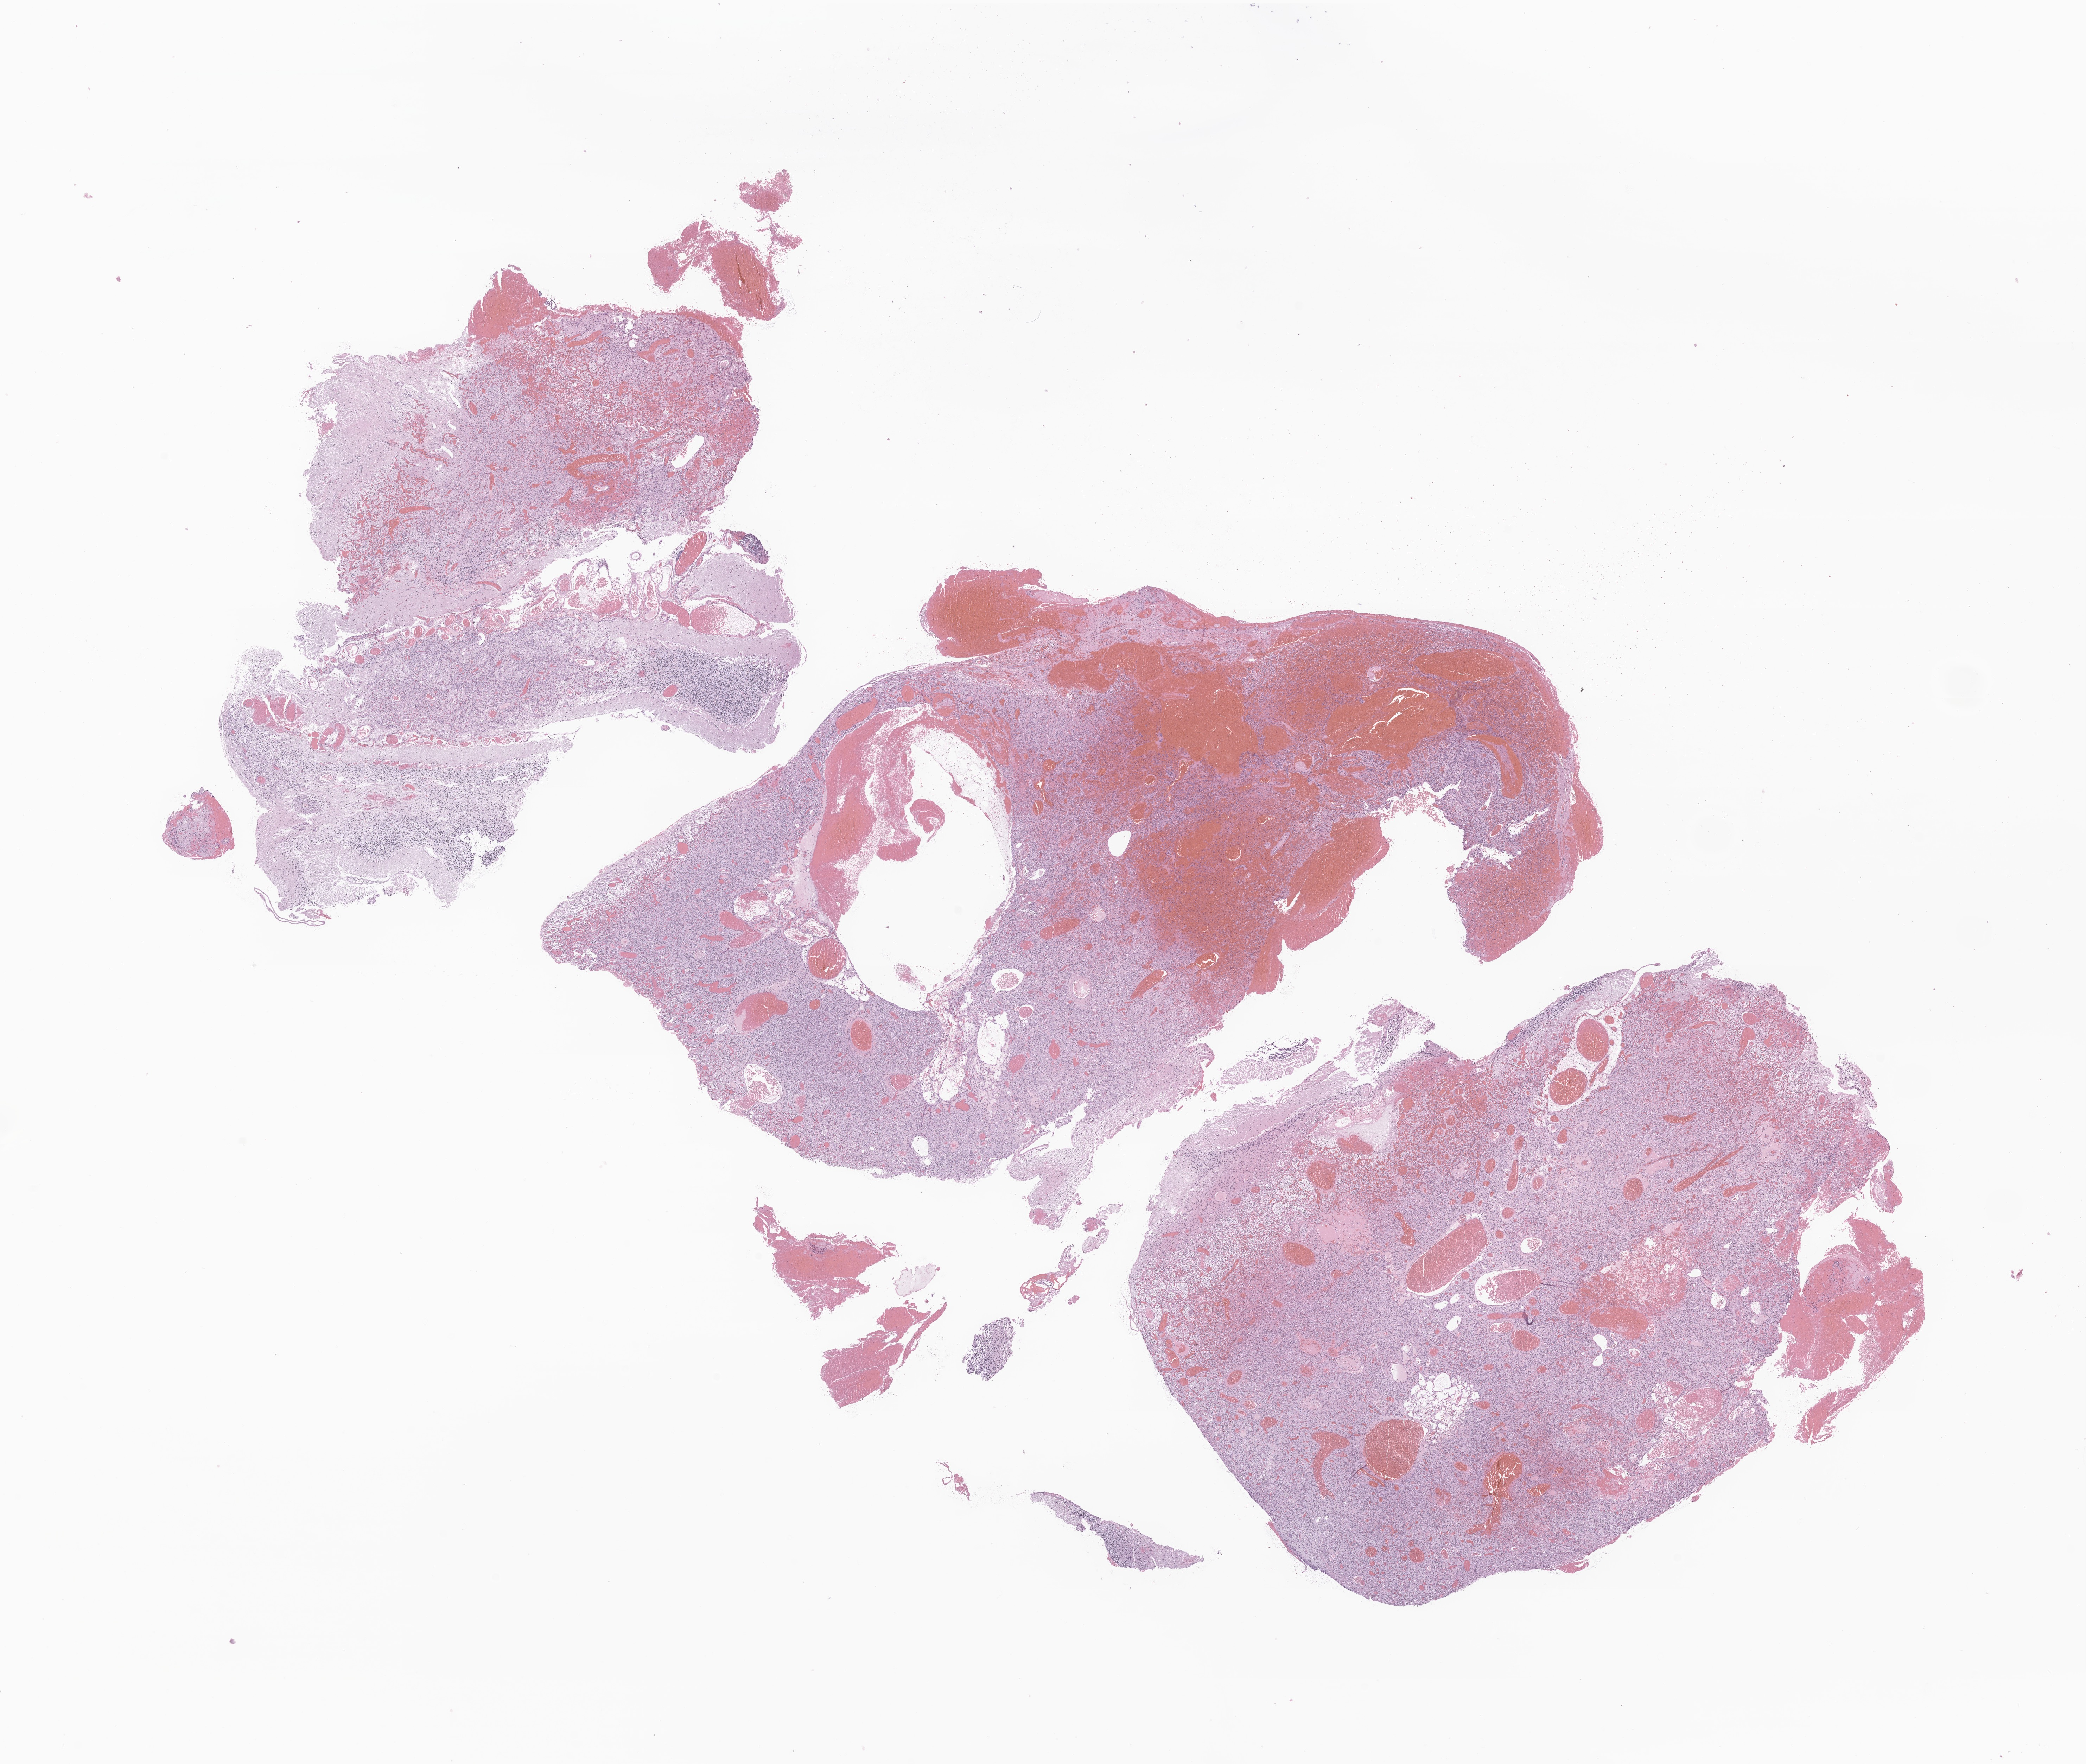
Whole-slide image, hematoxylin and eosin (H&E) stain of tumor tissue from the cerebellum — shown as a low-resolution overview of the whole scanned area (about 25.0 x 21.1 mm), formalin-fixed paraffin-embedded section. Male patient, age 209 months (17 years 5 months).
* diagnosis (ICD-O-3 morphology term): Hemangioblastoma